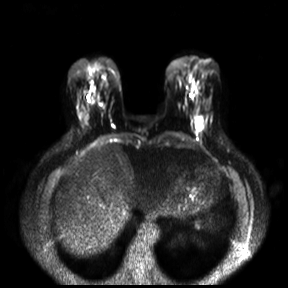
Breast MRI, one axial slice. Diffusion-weighted series; image 2 of 4 stored at this slice position (different b-values; order by instance number). 3 T. 4 mm slice thickness. 288 × 288 image matrix, field of view 360 × 360 mm. Female patient.
Structures marked on this image (expert manual segmentation):
- tumour on diffusion-weighted imaging: box from (x=196, y=119) to (x=202, y=129) px